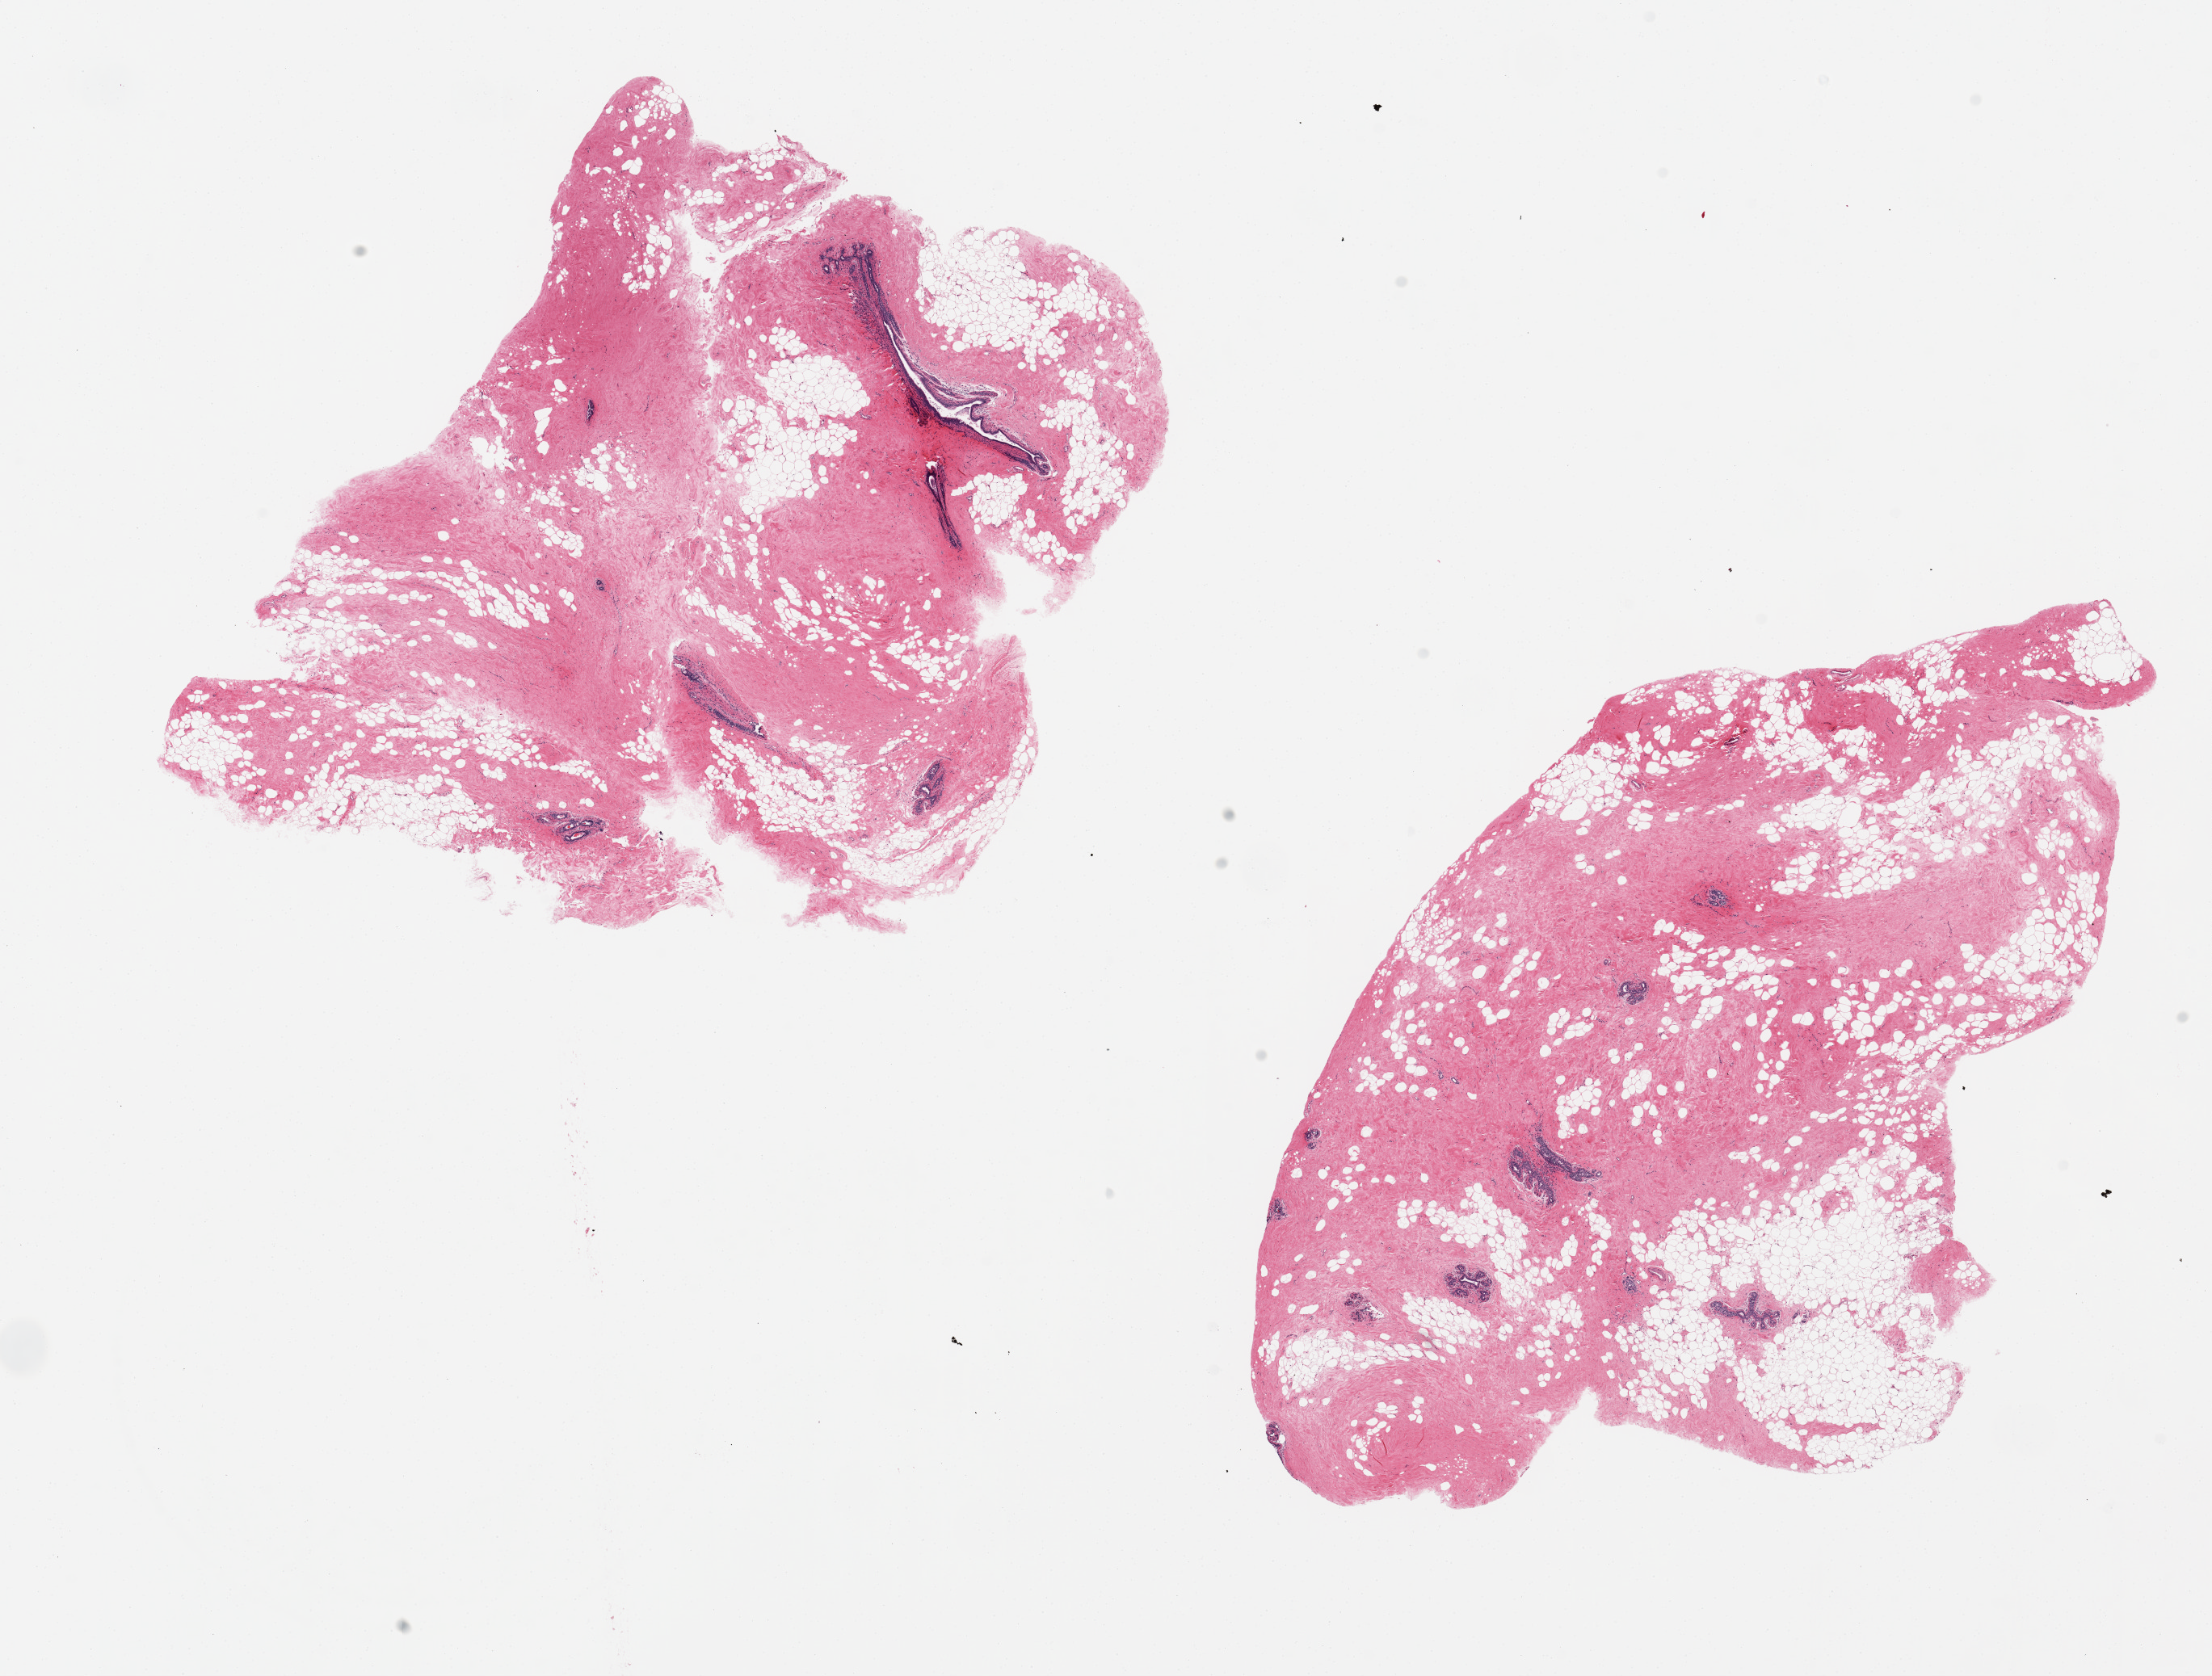
Whole-slide image, haematoxylin and eosin stain, a low-resolution overview of the entire scanned area, about 21.7 x 16.4 mm (acquisition: 20x scan), PAXgene-fixed paraffin-embedded (PFPE) section, sampled site (target tissue): breast, donor tissue sample.
Pathologist's review note for this sample: 2 pieces. 9x8 & 11x7mm; ductal lobular units in one; ducts in other; 40% adipose.